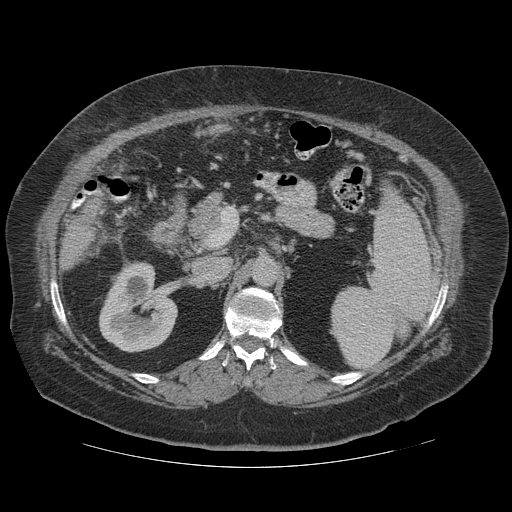
Contrast-enhanced abdominal CT (liver protocol), one axial slice. Slice 56 of 121 in the series (ordered by position). Soft-tissue window (W 400 / L 40 HU). 2.5 mm slice thickness. 512 × 512 image matrix, field of view 420 × 420 mm. From the clinical record (not read from this slice): diagnosis: hepatocellular carcinoma (patient treated with transarterial chemoembolisation; whether this scan precedes or follows treatment is not stated here); TNM stage (as recorded): Stage-IIIA; Child-Pugh class: A; tumour nodularity: multinodular; tumour size: 7.4 cm.
Structures marked on this image (semi-automatic segmentation, software-assisted and operator-edited):
- liver parenchyma outside the tumour (the mass and vessels are separate outlines, so this box may not span the whole liver): bounding box [x1, y1, x2, y2] px = [60, 224, 85, 270]